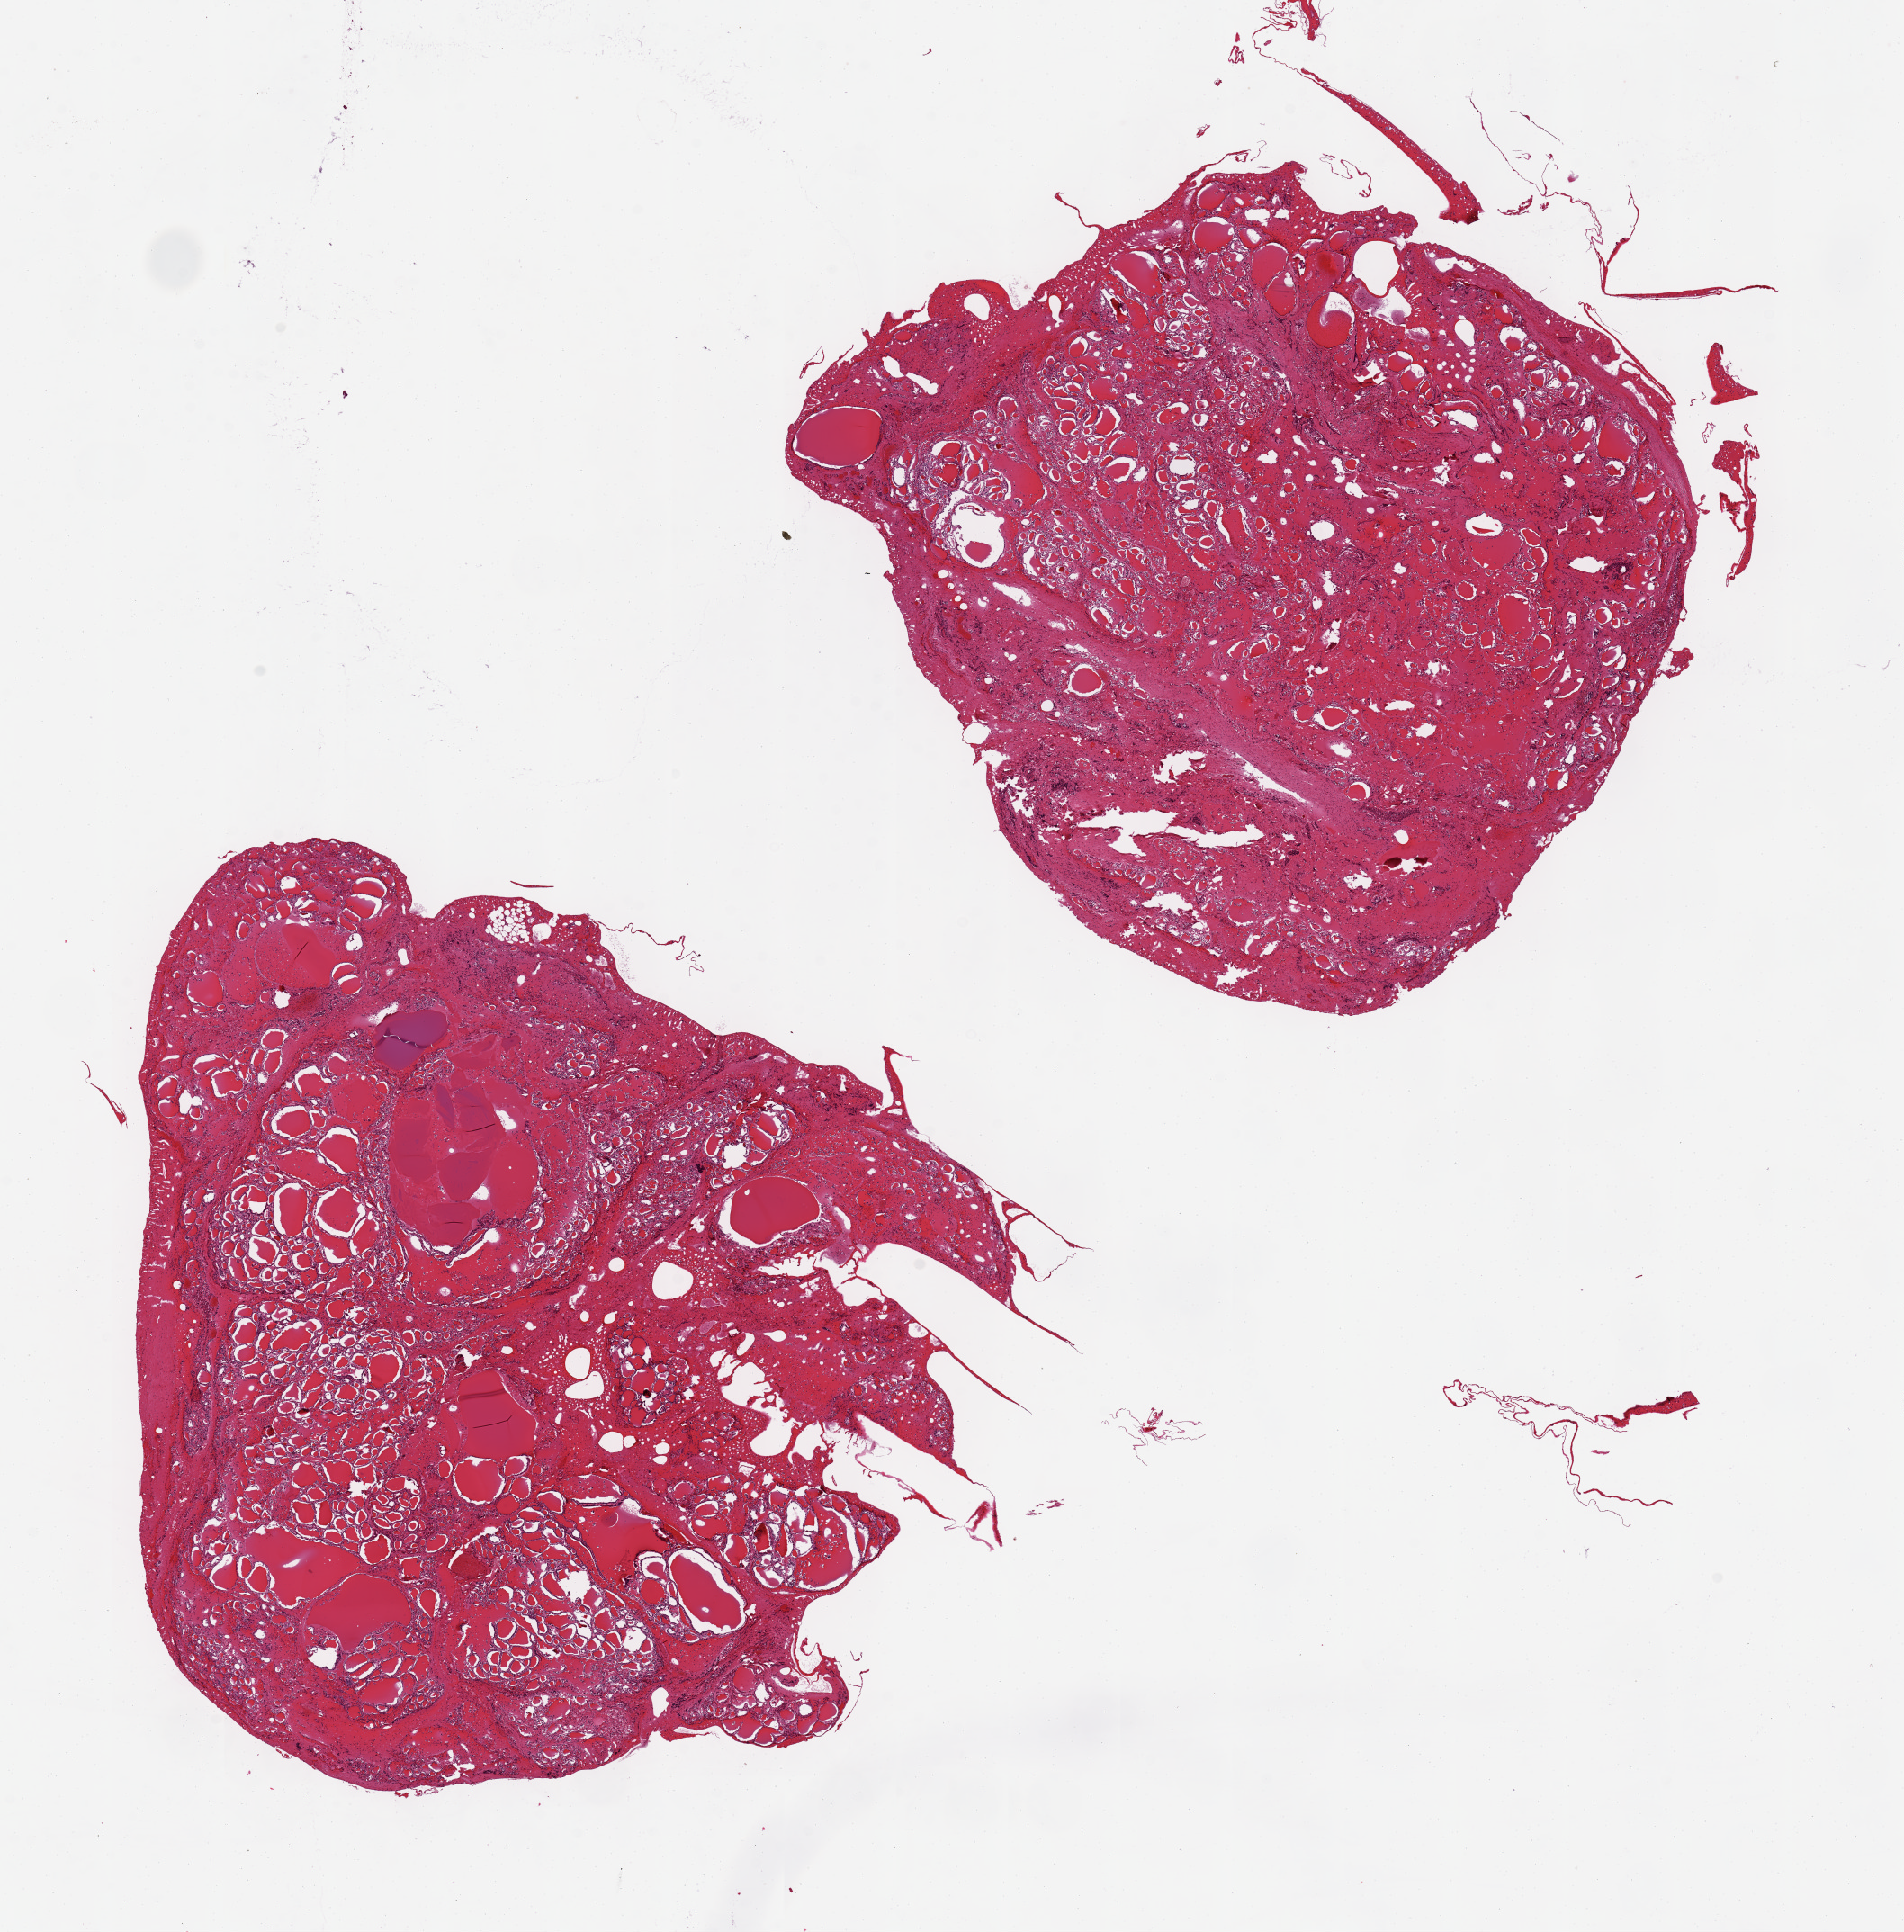
Whole-slide image, hematoxylin and eosin (H&E) stain, brightfield — whole scanned area (about 16.7 x 17.0 mm, acquisition: 20x scan) shown as a low-resolution overview. PAXgene-fixed paraffin-embedded (PFPE) section. Sampled site (target tissue): thyroid. Tissue donor sample. Donor: female.
Review note (as recorded): 2 pieces, 8x7 & 7x7 mm; partly nodular.